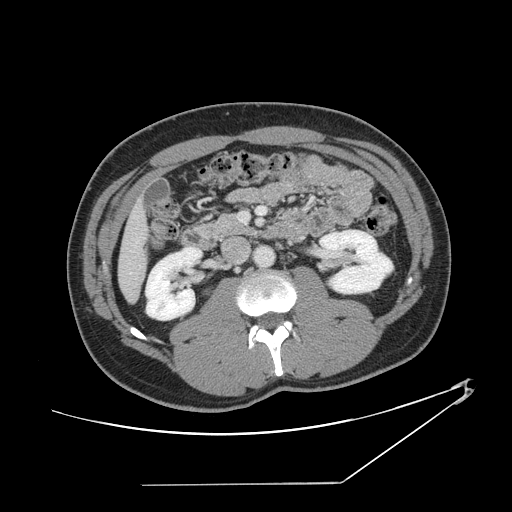
Contrast-enhanced abdominal CT, one axial slice; position 51 of 152 along the scan axis; intravenous contrast given; soft-tissue window (W 400 / L 40 HU); 2.5 mm slice thickness; 512 × 512 image matrix. Male patient, age 45 years. From the clinical record (not read from this slice): diagnosis: colorectal cancer liver metastases, imaged before liver resection; multiple liver metastases: no; largest metastasis: 1 cm.
Outlined on this slice (outlined manually by an expert reader):
- hepatic veins: bounding box <134,239,139,248> (left, top, right, bottom; pixels)
- liver: <119,207,146,301>
- planned liver remnant (the part of the liver to remain after resection): <119,207,146,301>
- portal vein (with intrahepatic branches): <241,207,266,222>